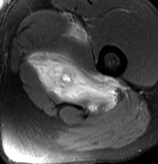
MRI of an extremity soft-tissue mass, one axial slice; slice 64 of 70 in the series (ordered by position); T2-weighted fat-saturated; MR volume resampled by the dataset authors to the PET/CT grid (not the native acquisition matrix); 3.27 mm slice thickness; 158 × 164 image matrix, field of view 154 × 160 mm. Male patient. From the clinical record (not read from this slice): histological type: extraskeletal osteosarcoma; grade: high; site of the primary tumour: left adductur.
Structures marked on this image (expert contour drawn on MRI and transferred to this co-registered scan by the dataset authors):
- gross tumour volume (mass): box from (x=27, y=19) to (x=126, y=113) px